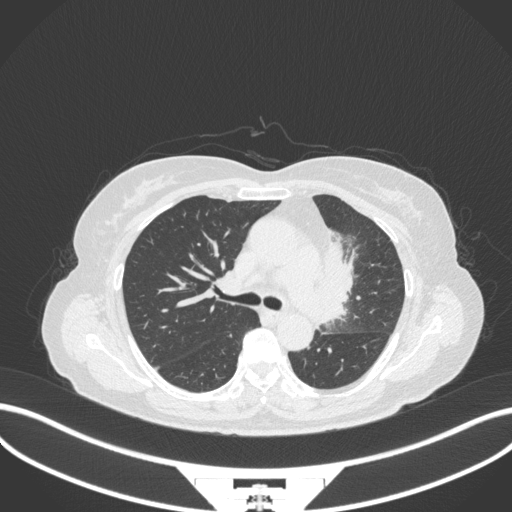
Chest CT, one axial slice. Slice 214 of 382 in the series (ordered by position). Reconstruction kernel B31f. 120 kVp. Lung window (W 1500 / L -600 HU). 1 mm slice thickness. 512 × 512 image matrix, field of view 400 × 400 mm. Patient: female, 64 years. Case-level facts recorded for this patient, not image findings: clinical TNM (as recorded): T2a N2 M0.
Structures marked on this image (bounding box drawn by a radiologist):
- lung tumour (recorded histology: adenocarcinoma): box from (x=325, y=230) to (x=357, y=322) px